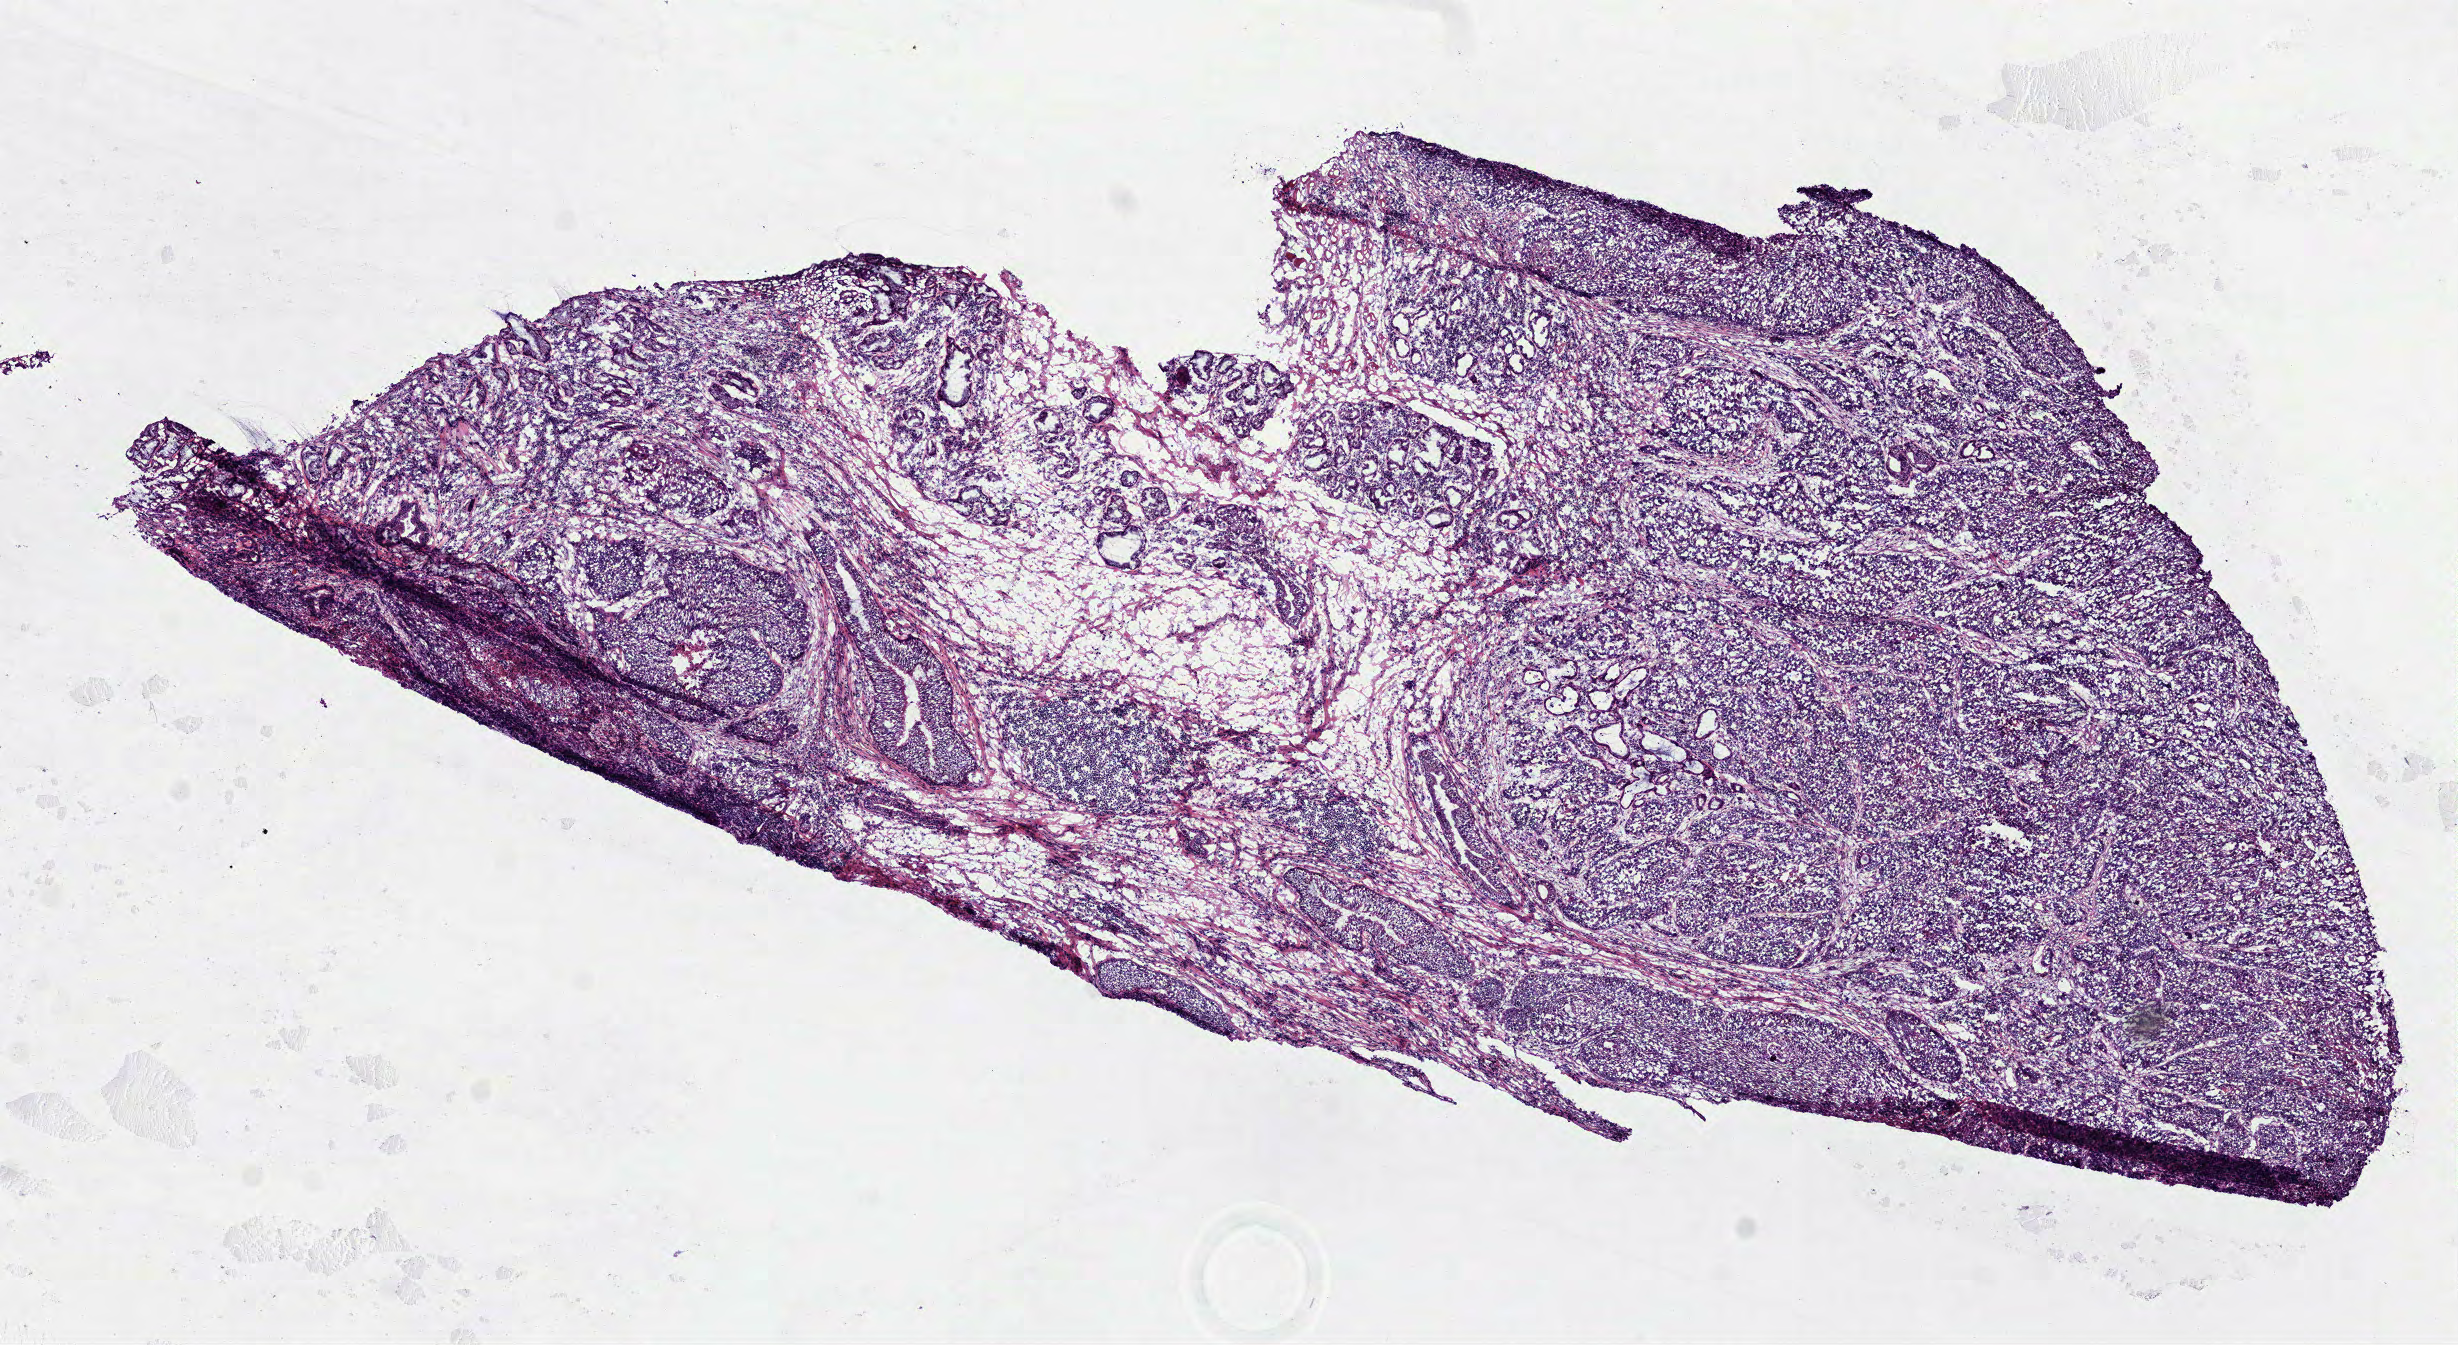
Hematoxylin and eosin (H&E) stained whole-slide image, a low-resolution overview of the entire scanned area, about 9.9 x 5.4 mm; frozen section from the top of the tissue portion; head and neck, primary tumour sample. Patient: male, age at initial diagnosis 53 years. Histologic grade: G2 (moderately differentiated). Composition of this section per pathologist review: tumour cells 85%, tumour nuclei 75%, normal cells 0%, stromal cells 15%, necrosis 0%.
Pathologic diagnosis: Squamous cell carcinoma, NOS (larynx, NOS). AJCC pathologic stage: IVA.